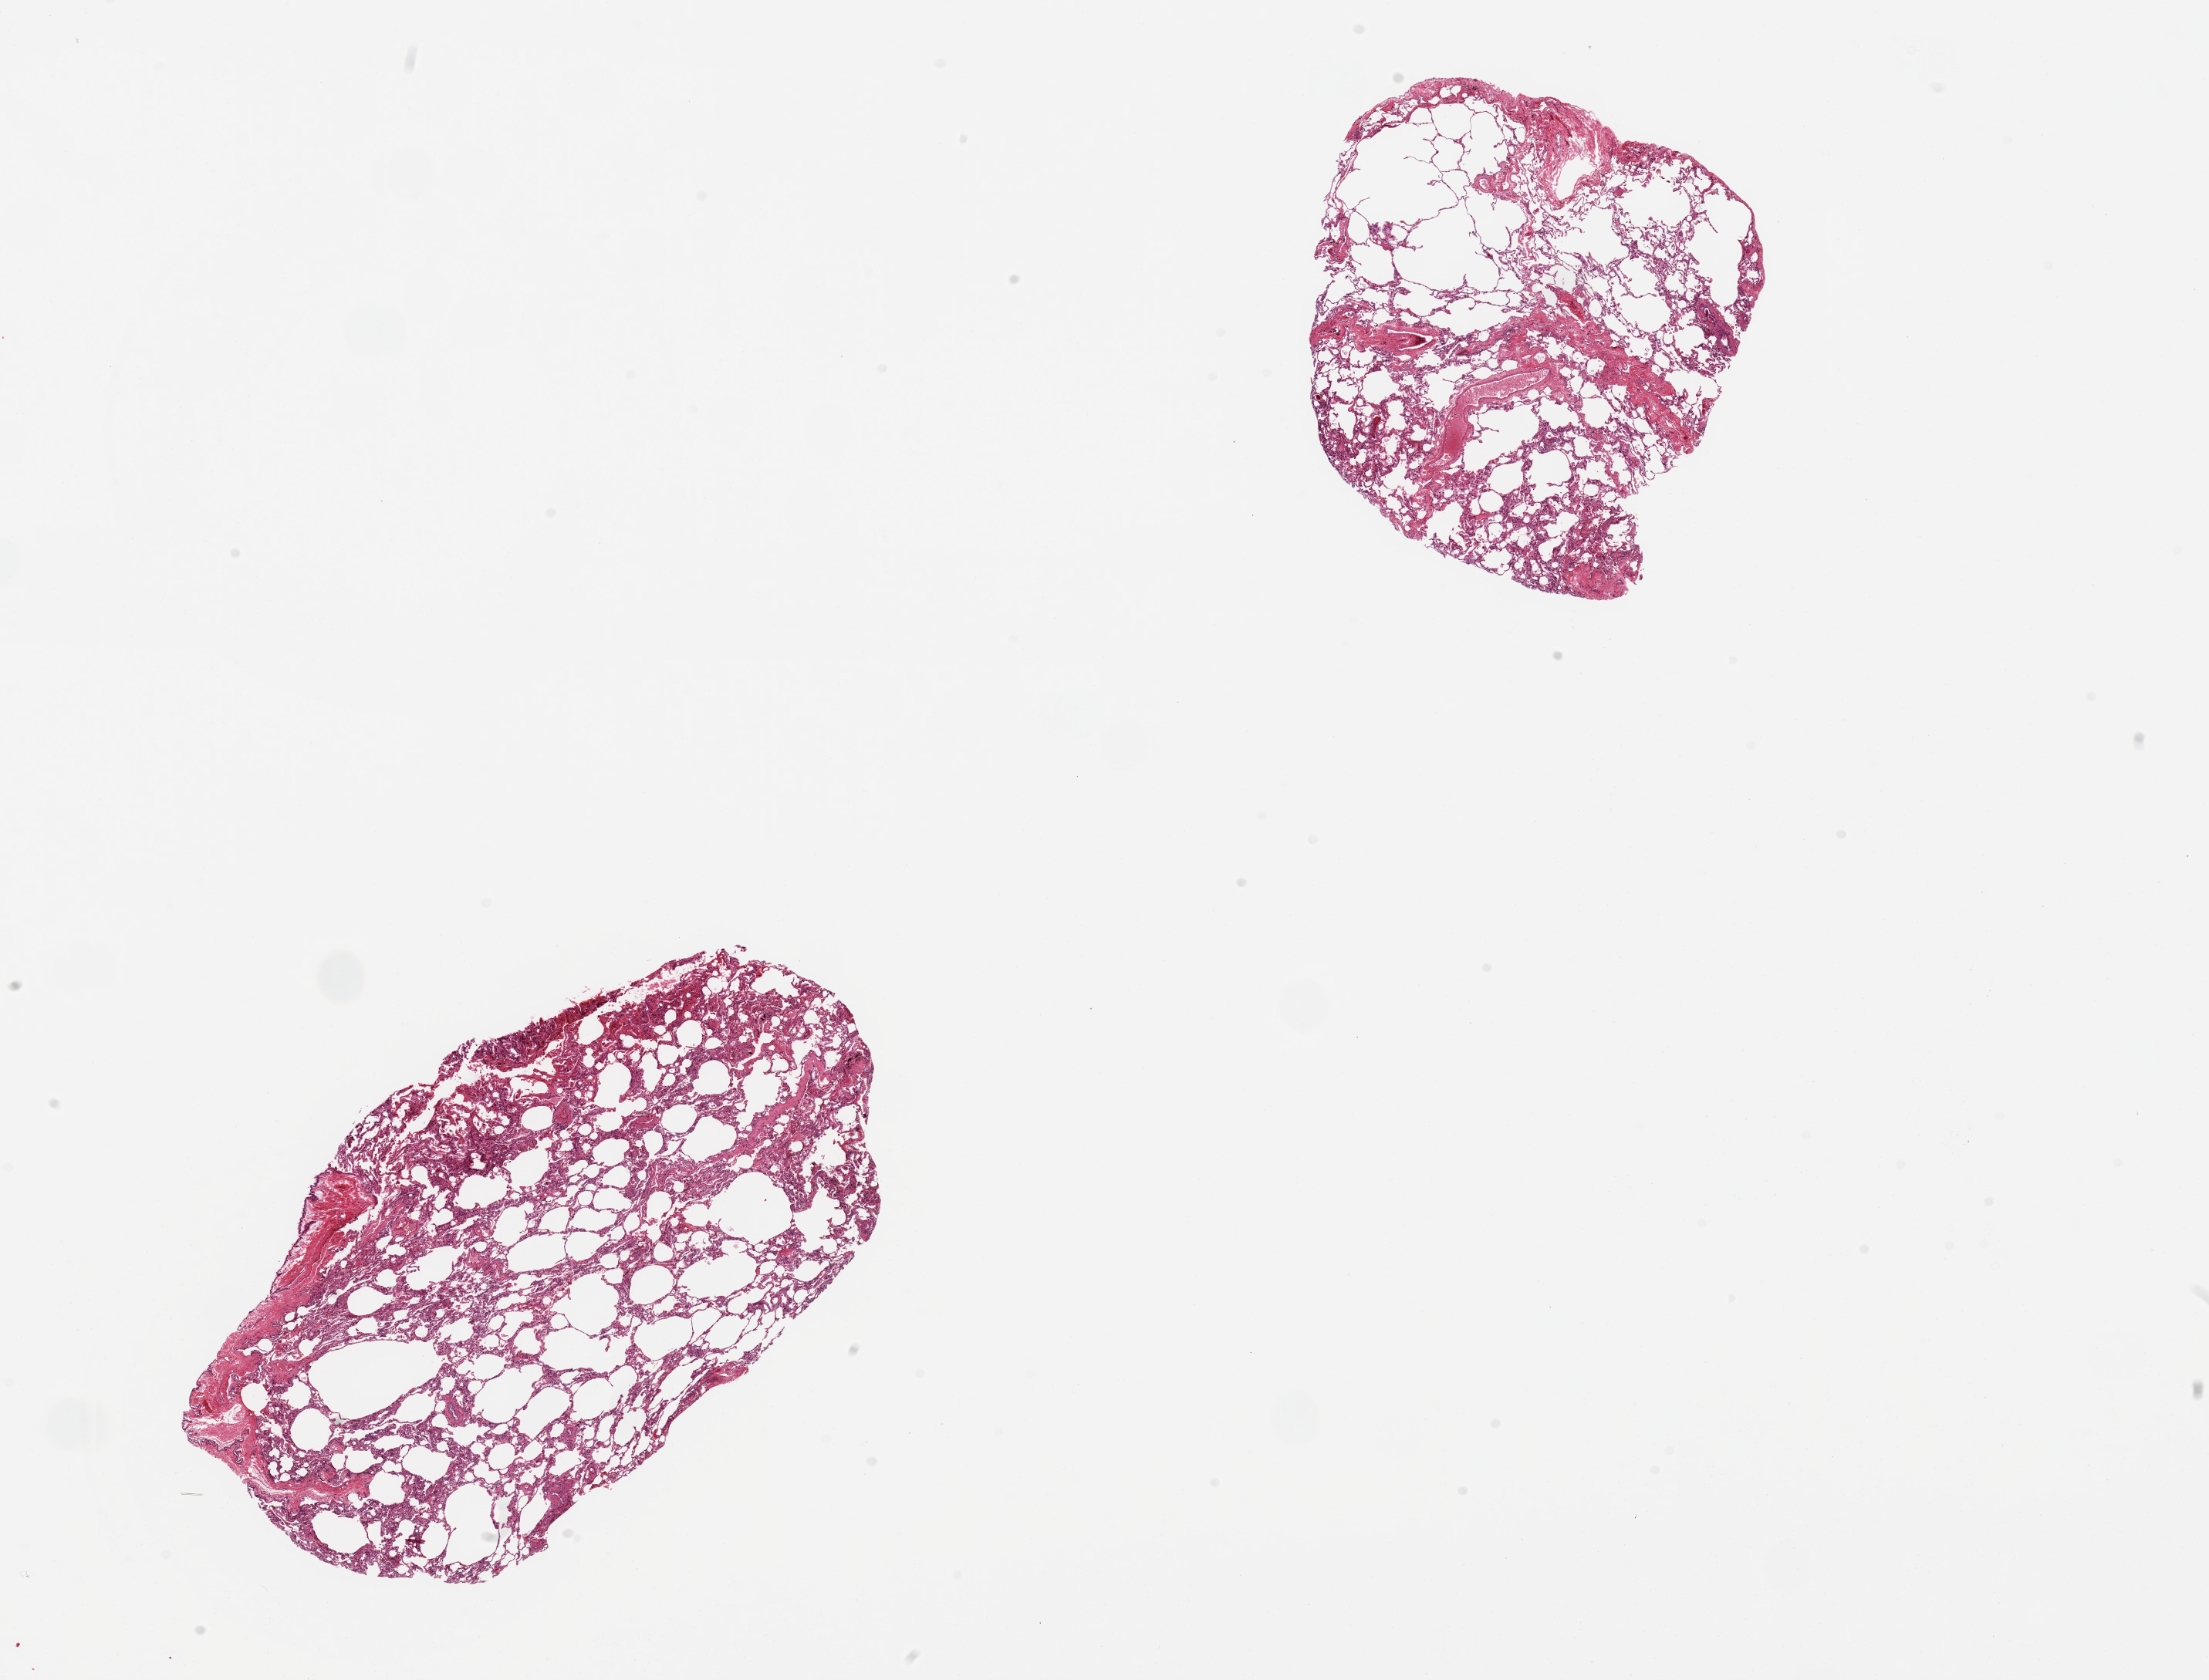
Digitized haematoxylin and eosin-stained section, brightfield, shown as a low-resolution overview of the whole scanned area (about 22.6 x 17.2 mm, from a 20x scan); PAXgene-fixed, paraffin-embedded tissue; target tissue: lung; donor tissue sample.
• reviewer comment on this tissue sample: 2 ~6.5x5mm pieces. Well preserved; no inflammation; pronounced emphasymatous changes